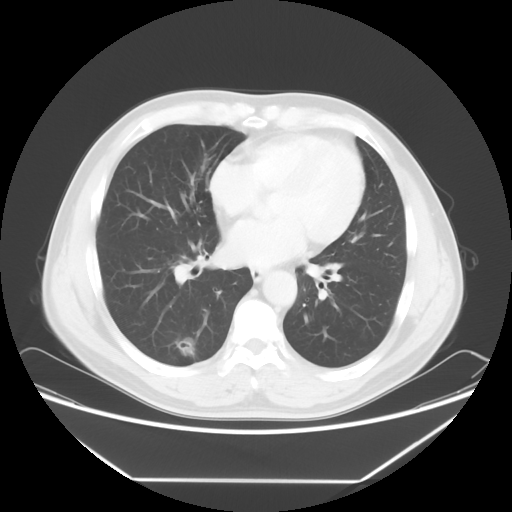
Chest CT, one axial slice. Slice 29 of 65 in the series (ordered by position). 120 kVp. Lung window (W 1500 / L -600 HU). 5 mm slice thickness. 512 × 512 image matrix, field of view 418 × 418 mm. Patient: male, 50 years. Case-level facts recorded for this patient, not image findings: clinical TNM (as recorded): T1c N0 M0.
Structures marked on this image (rectangle marked by the reading radiologist):
- lung tumour (recorded histology: adenocarcinoma): bounding box (x1, y1, x2, y2) in pixels: (171, 333, 199, 363)